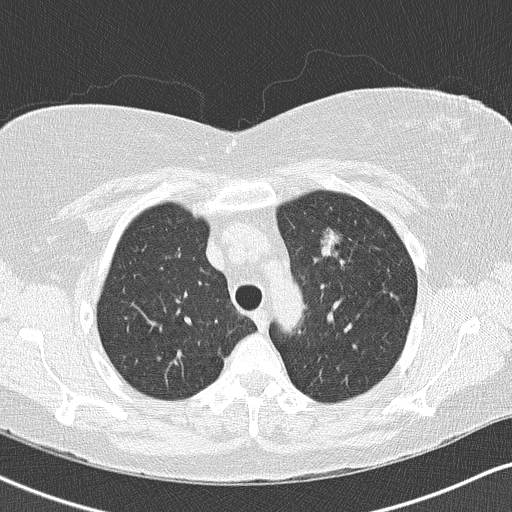
Low-dose screening chest CT, one axial slice; reconstruction kernel B50f; 120 kVp; lung window (W 1500 / L -600 HU); 2 mm slice thickness; 512 × 512 image matrix, field of view 328 × 328 mm.
Structures marked on this image (outlined manually by an expert reader):
- lesion 1 (tumor, upper lobe of left lung): bounding box <320,227,342,258> (left, top, right, bottom; pixels)